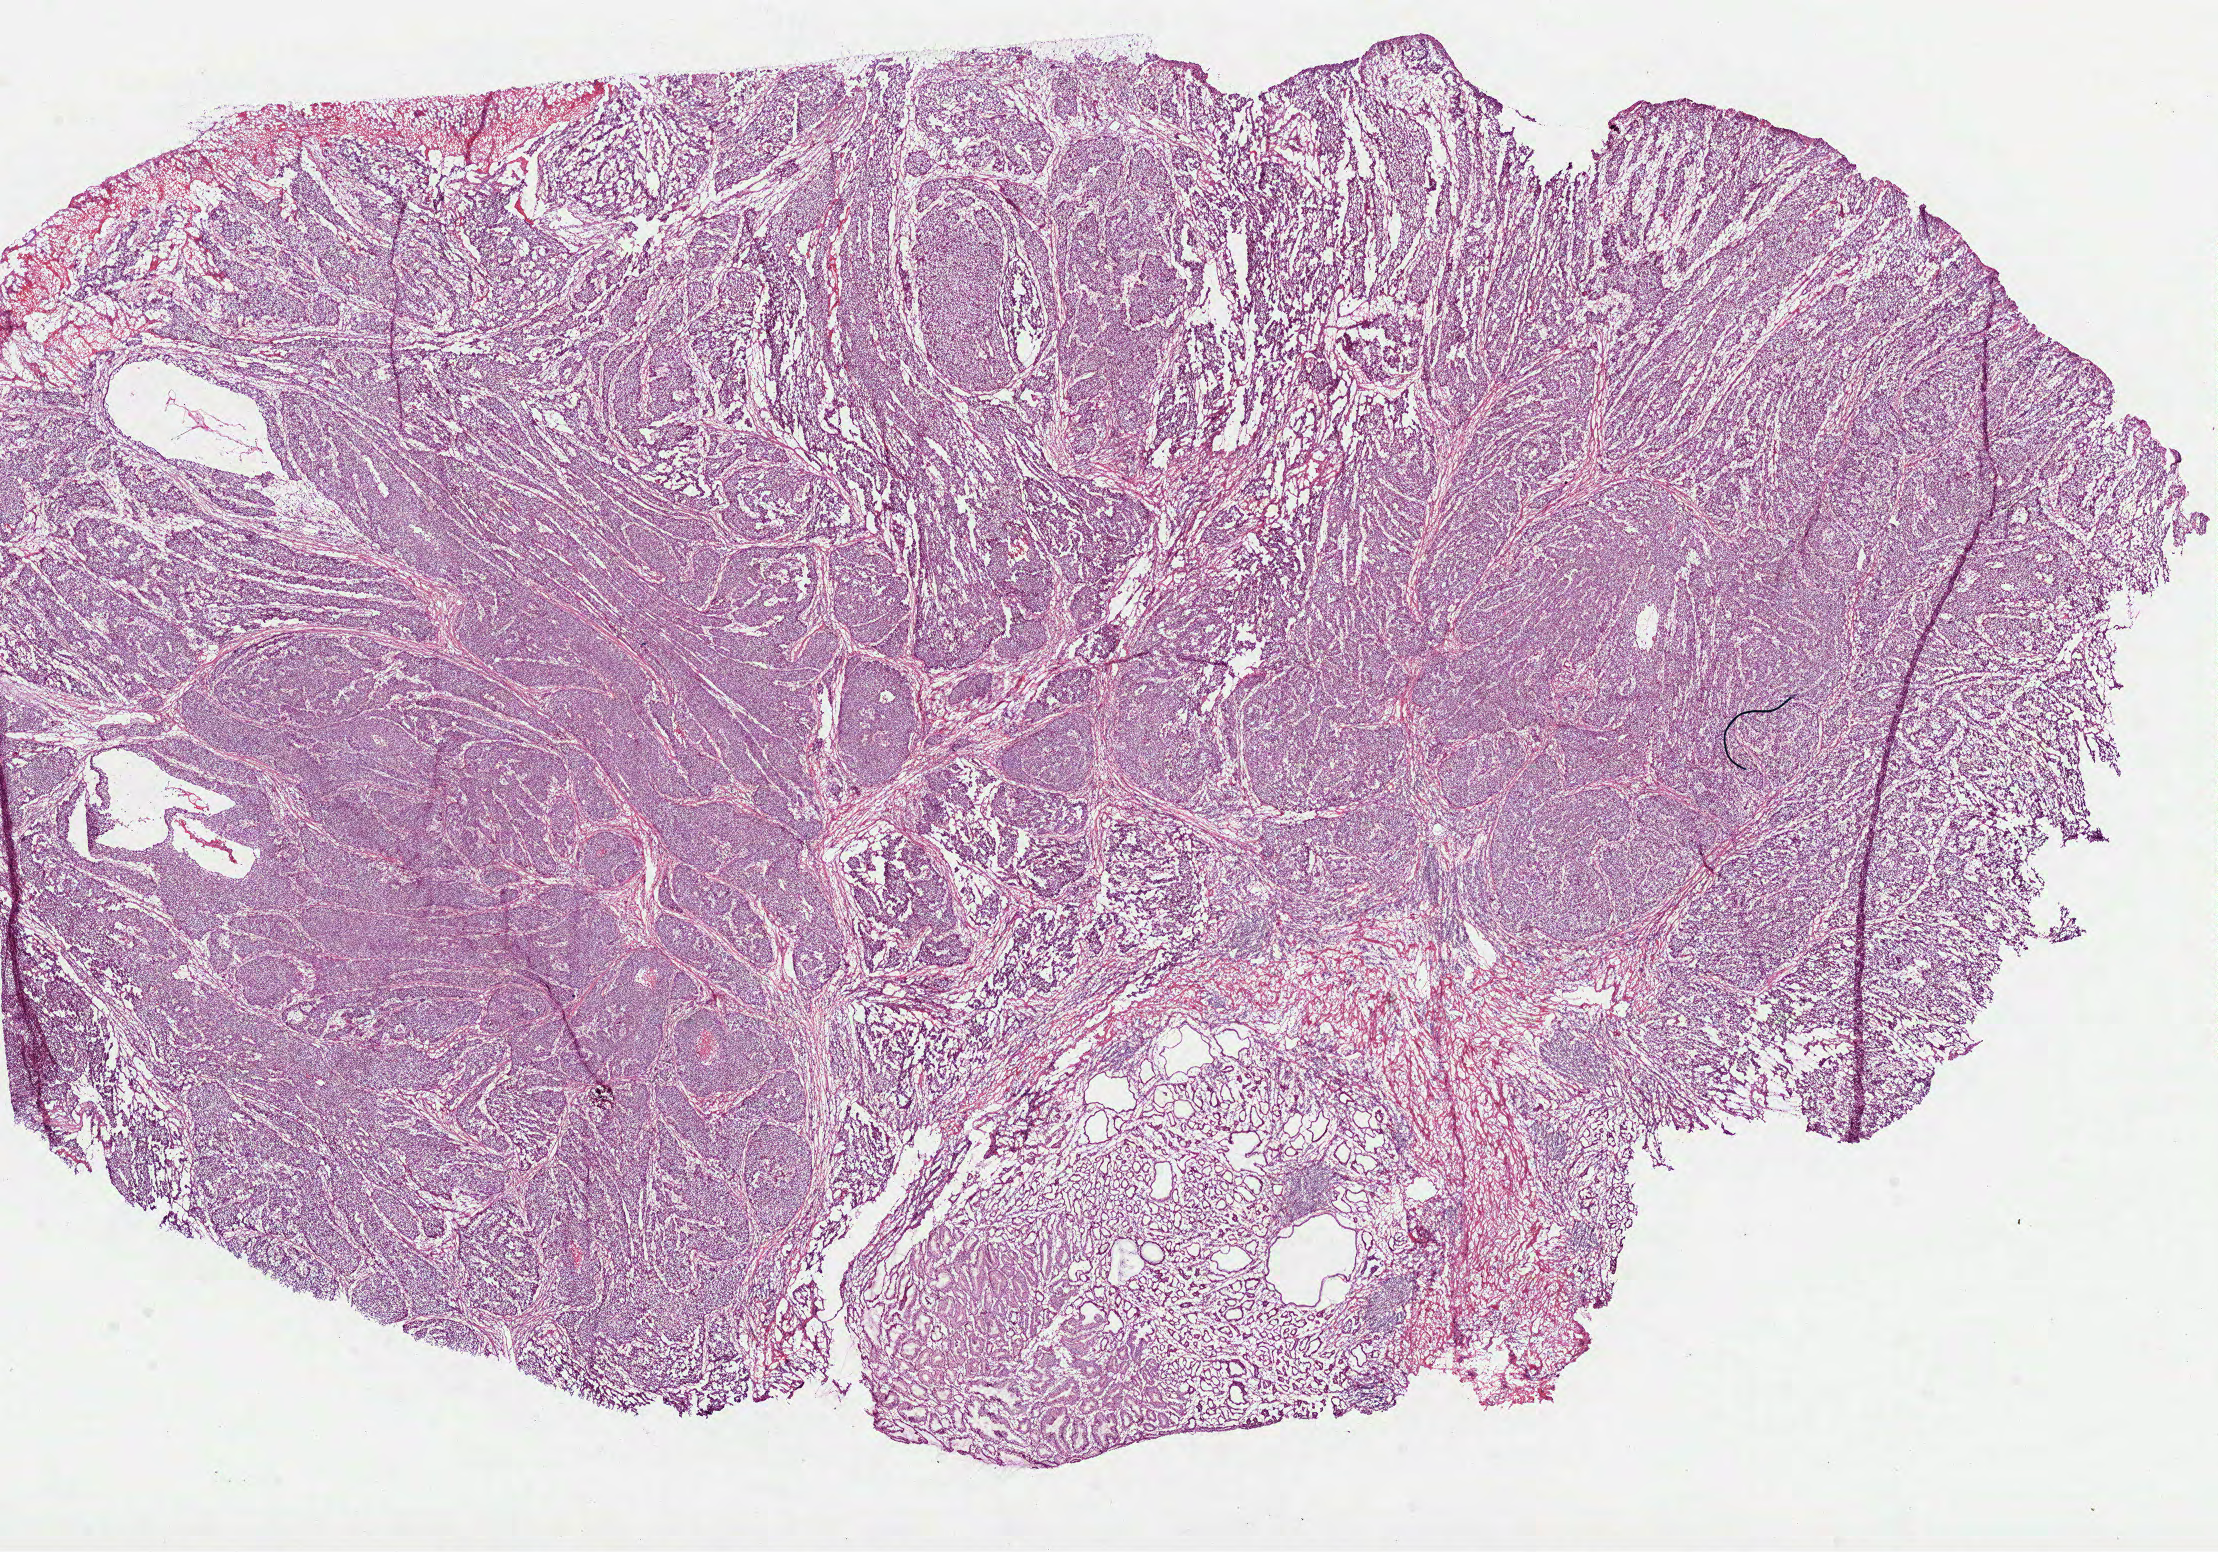
H&E whole-slide image, low-resolution overview of the scanned area, about 17.9 x 12.5 mm; frozen section from the top of the tissue portion; stomach, primary tumour sample. Female, age 69 years at initial diagnosis. Histologic grade: G3 (poorly differentiated). Slide review estimates, as recorded: tumour cells 80%, tumour nuclei 70%, normal cells 5%, stromal cells 10%, necrosis 5%.
Lymph nodes positive (case pathology): 0 of 3 examined. Histologic diagnosis: Adenocarcinoma, intestinal type (body of stomach). AJCC pathologic stage: II.